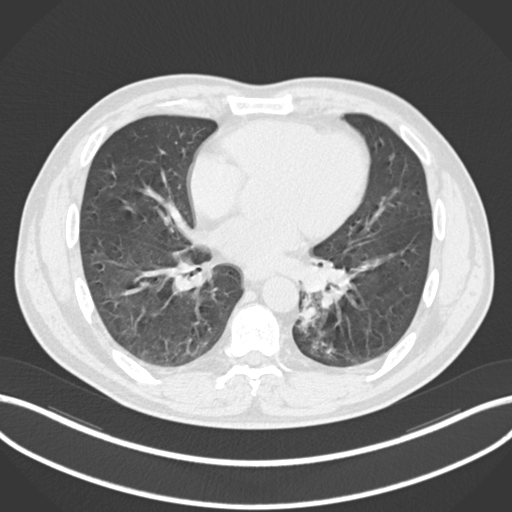
Chest CT, one axial slice; slice 95 of 223 in the series (ordered by position); reconstruction kernel B30f; lung window (W 1500 / L -600 HU); 512 × 512 image matrix, field of view 400 × 400 mm. Male patient, age 50 years. From the clinical record (not read from this slice): clinical TNM (as recorded): T2a N3 M0.
Annotated regions visible in this slice (rectangle marked by the reading radiologist):
- lung tumour (recorded histology: squamous cell carcinoma): bounding box <295,302,320,336> (left, top, right, bottom; pixels)